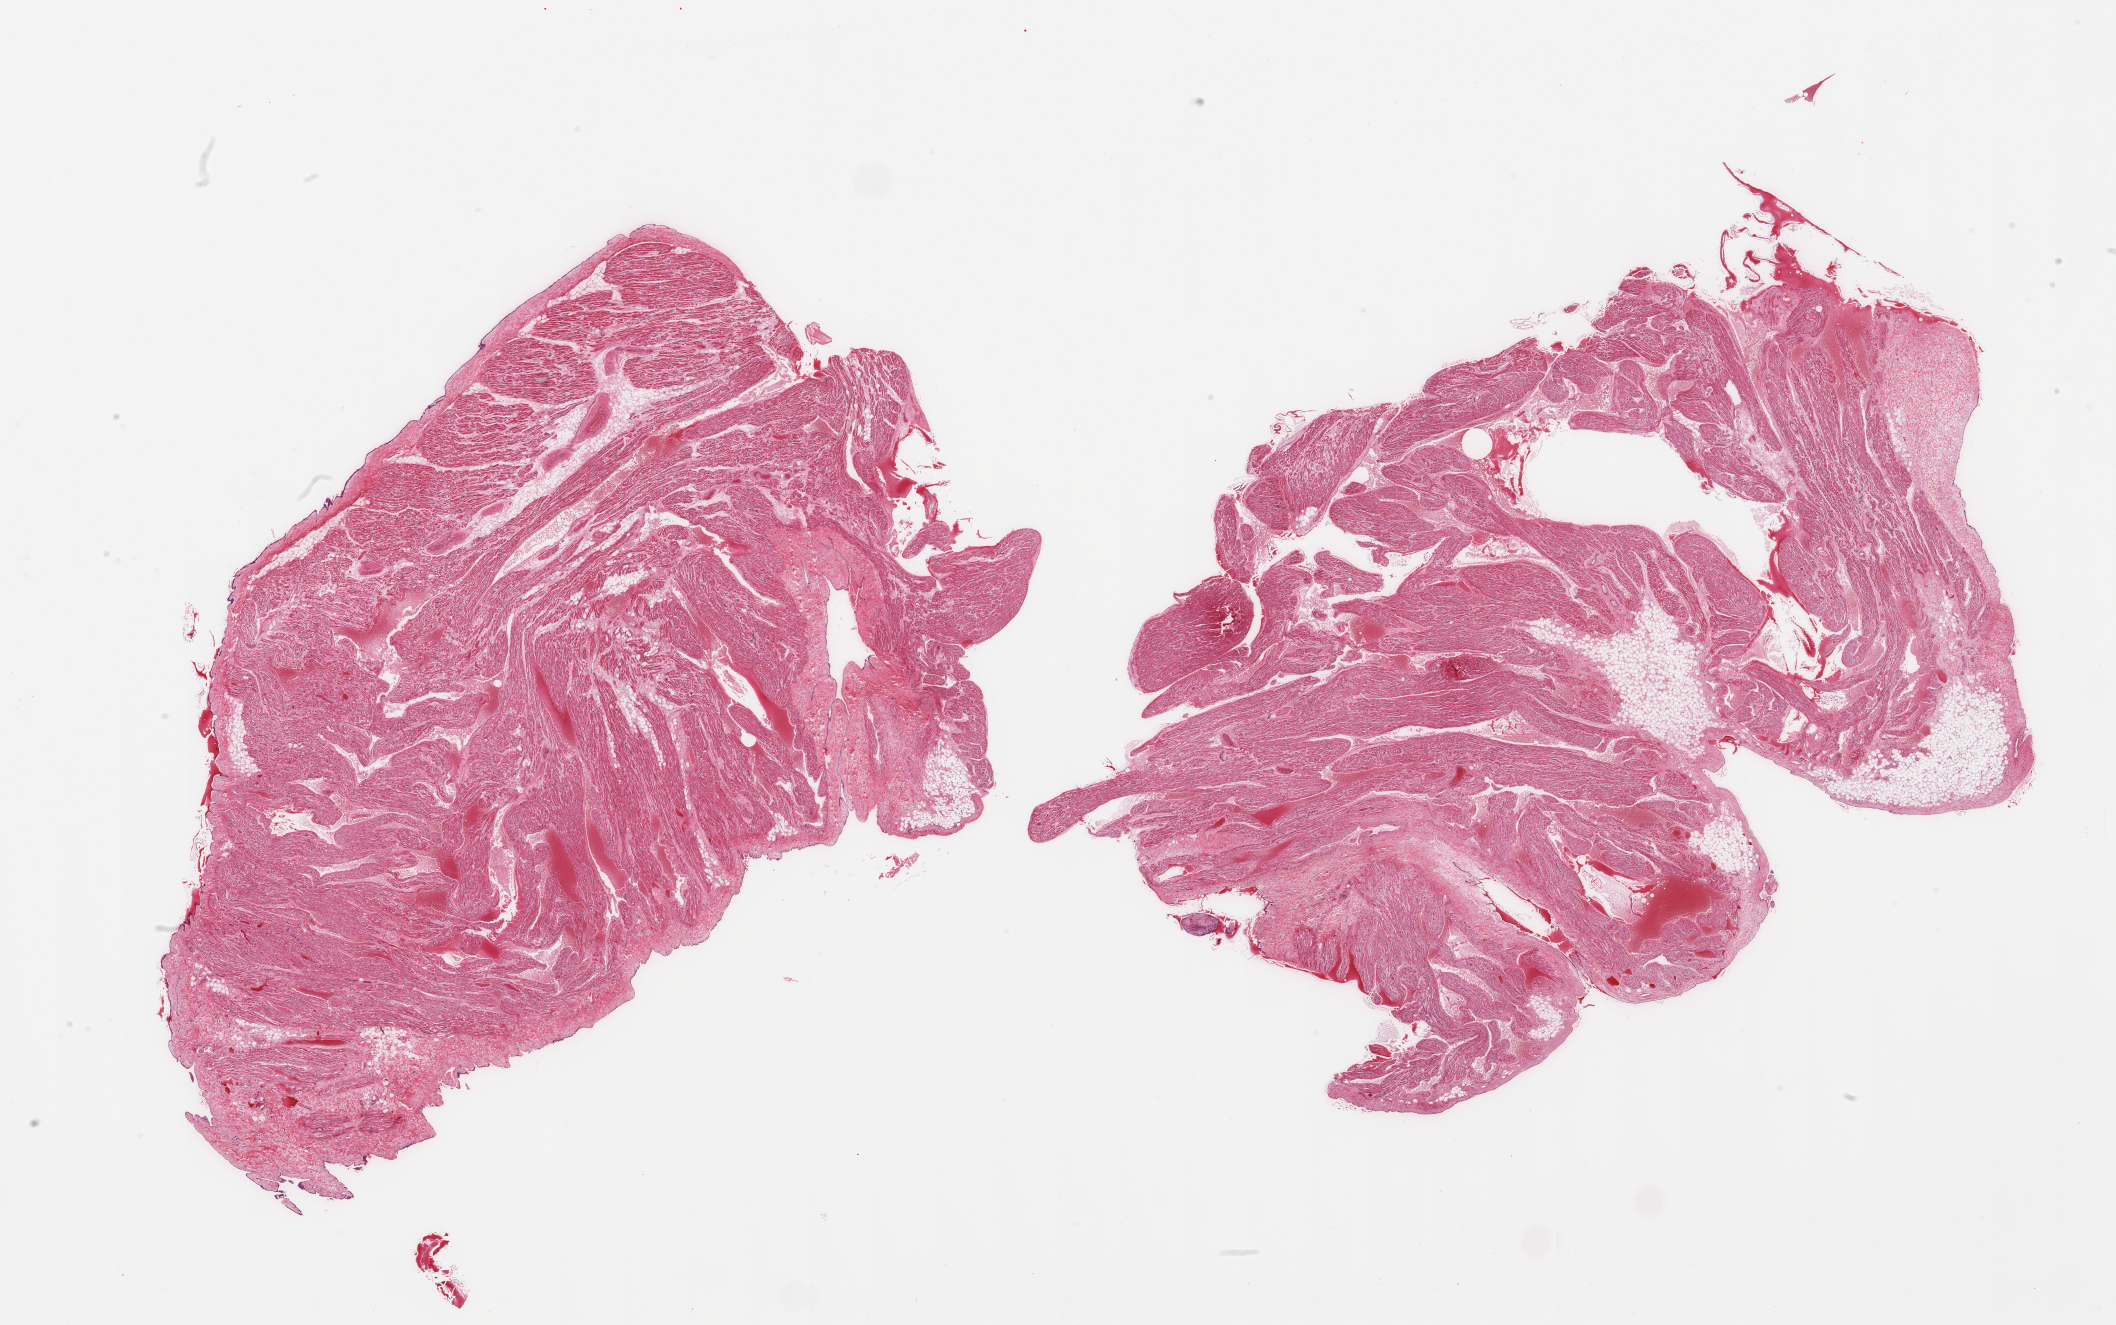
Digitized H&E-stained section — a low-resolution overview of the entire scanned area, about 33.5 x 21.0 mm; PAXgene-fixed paraffin-embedded (PFPE) section; sampled site (target tissue): auricular appendage; tissue donor sample.
• reviewer comment on this tissue sample: 2 pieces; 20-30% is fat/fibrous